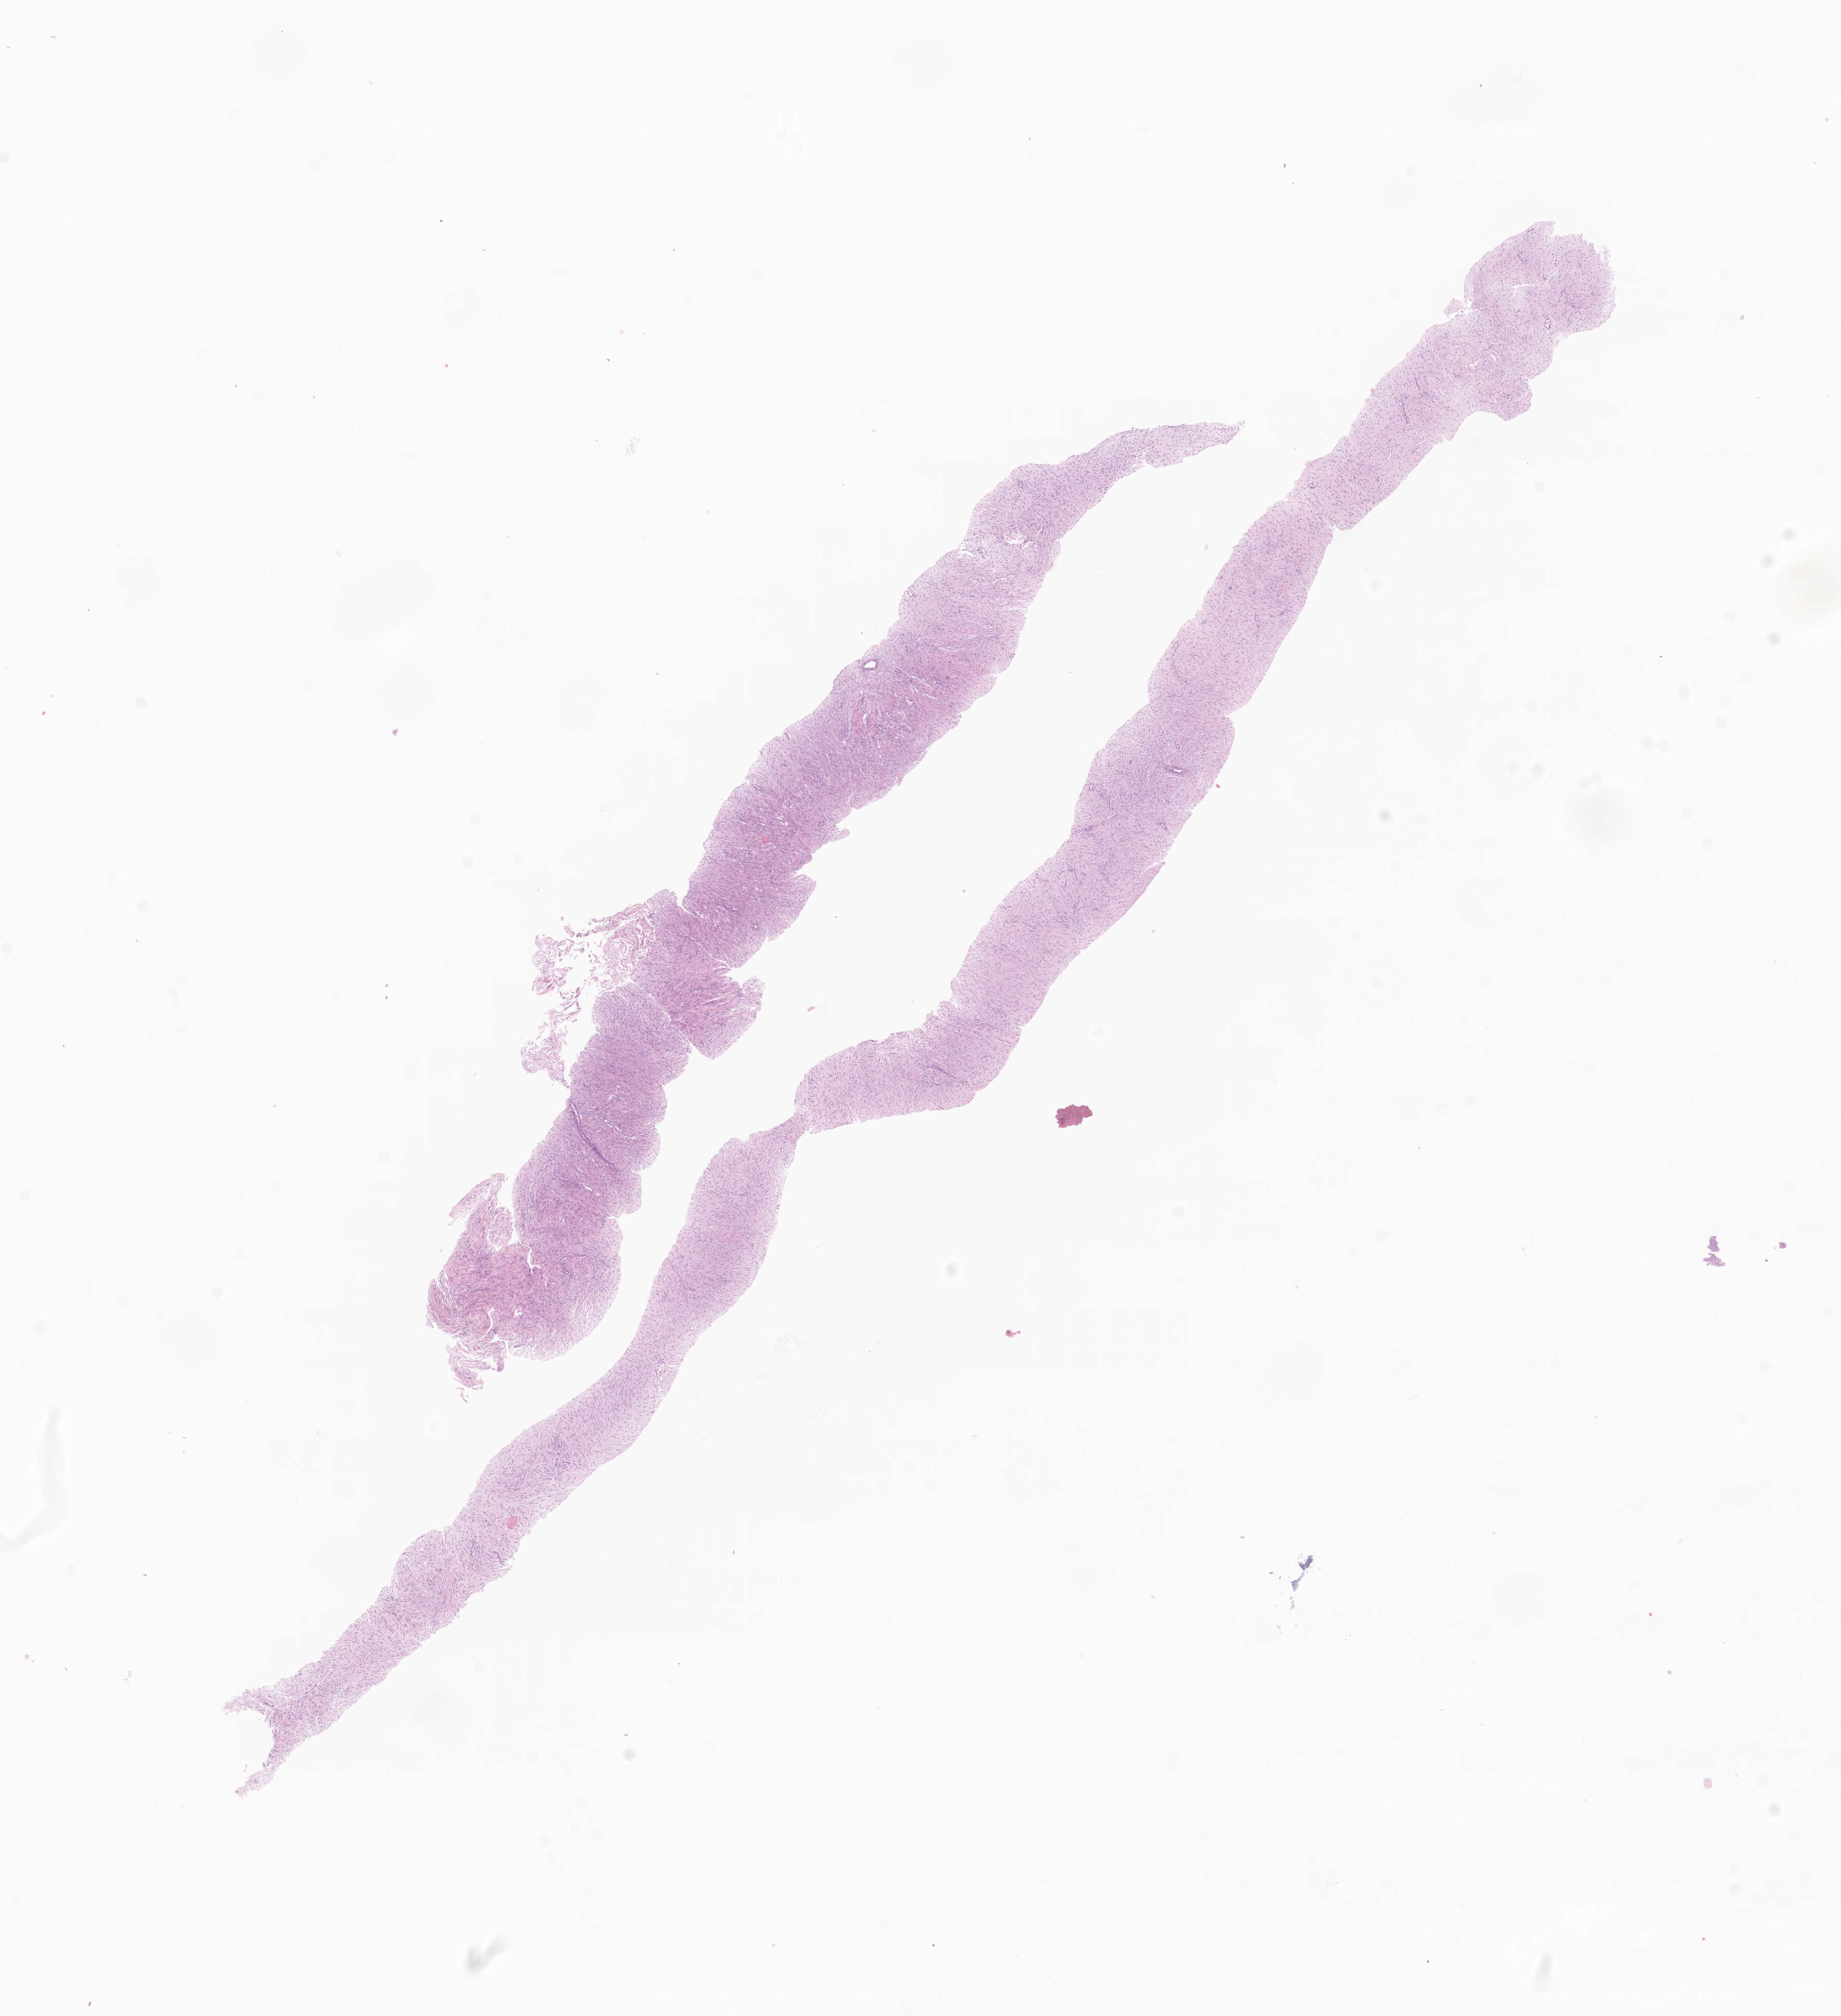
Hematoxylin and eosin (H&E) whole-slide image of tumor tissue from the soft tissues of head and neck — a low-resolution overview of the entire scanned area, about 15.1 x 16.5 mm, formalin-fixed, paraffin-embedded (FFPE) tissue. Female patient, age 853 days.
Diagnosis: Aggressive fibromatosis.